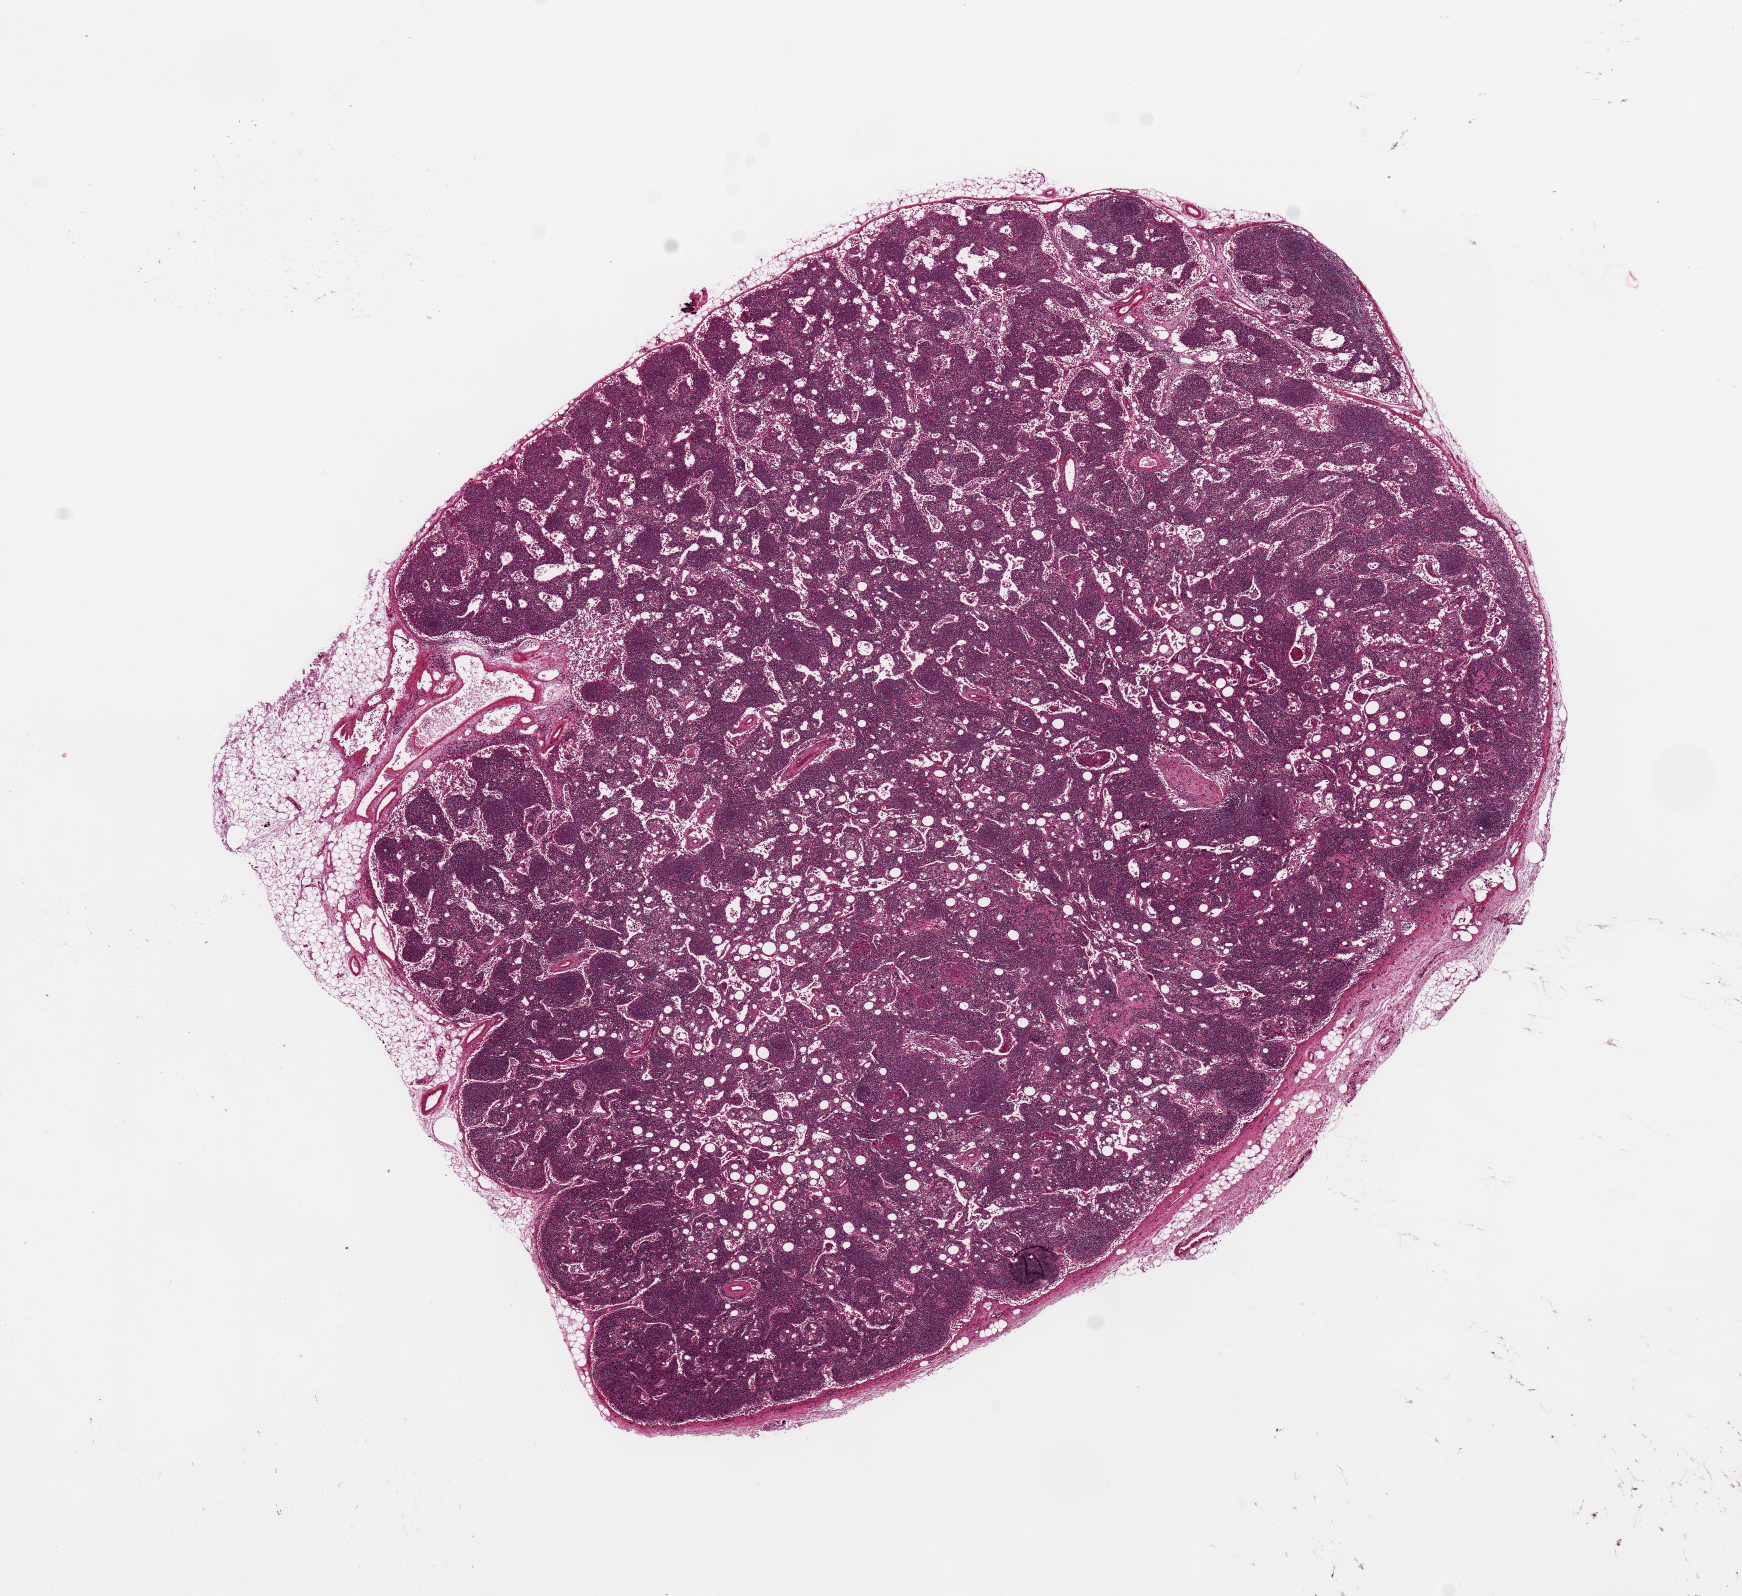
Digitized H&E-stained section, shown as a low-resolution overview of the whole scanned area (about 13.8 x 12.6 mm); PAXgene-fixed, paraffin-embedded tissue; target tissue: thyroid; tissue donor sample. Female donor.
Review note (as recorded): 8x7mm- Not thyroid???capsule and peripheral sinuses; favor lymph node.